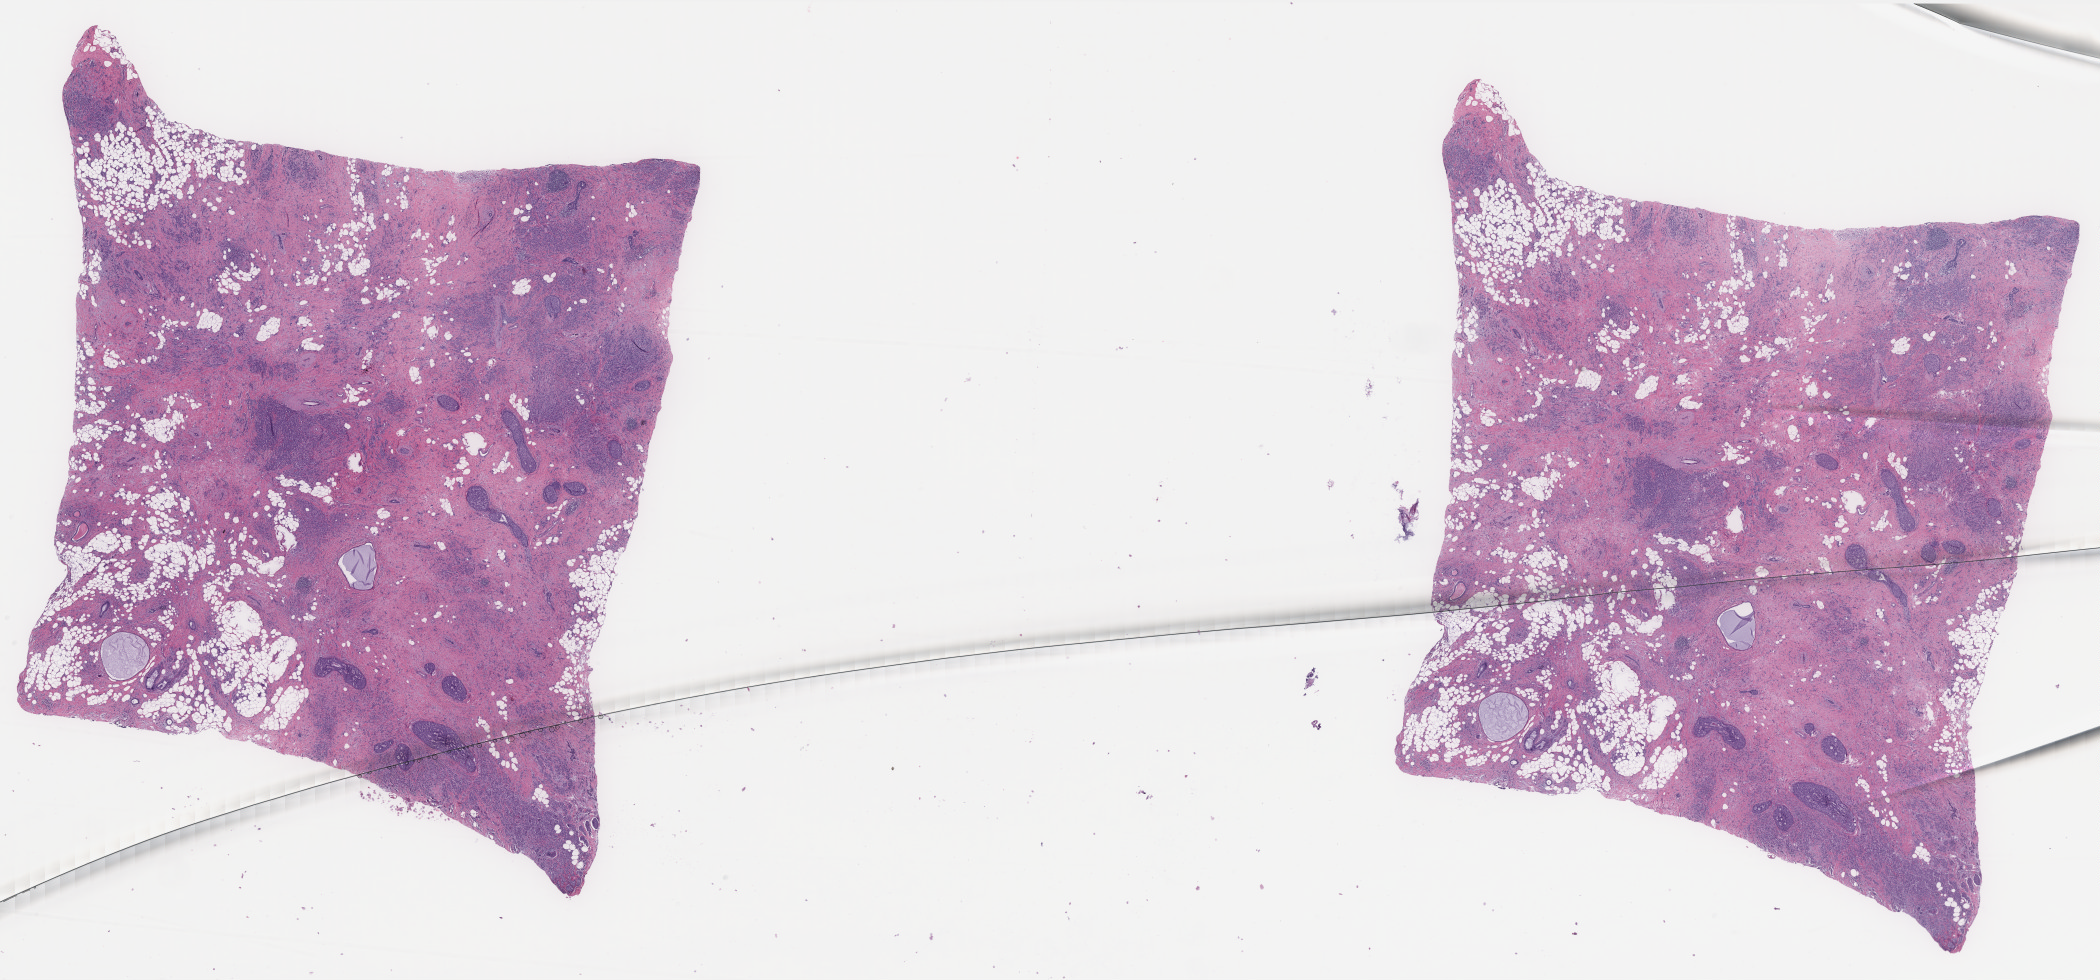
Whole-slide histology image, H&E-stained — a low-resolution overview of the entire scanned area, about 33.7 x 15.7 mm. FFPE section. Sample: primary tumour, breast. Female, age 62 years at initial diagnosis.
AJCC pathologic stage: I (6th edition). Diagnosis: Infiltrating duct and lobular carcinoma.